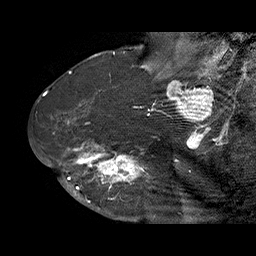
Breast MRI (dynamic contrast-enhanced), one sagittal slice. Slice 43 of 70 in the series (ordered by position). Dynamic contrast-enhanced series, time point 2 of 6 at this slice position (early post-contrast). 1.5 T. TE 4.5 ms, TR 32.4 ms. 3 mm slice thickness. 256 × 256 image matrix, field of view 180 × 180 mm. Female patient. Case-level facts recorded for this patient, not image findings: setting: breast cancer imaged before/during neoadjuvant chemotherapy; receptor status: HR-positive, HER2-negative.
Outlined on this slice (semi-automatically segmented with operator editing):
- analysis volume of interest (the breast-tissue region the enhancement analysis was run in; not a lesion): bounding box [x1, y1, x2, y2] px = [71, 128, 159, 202]
- tumour enhancement mask (voxels above the 100 % enhancement threshold inside the analysis volume of interest): [71, 142, 149, 202]